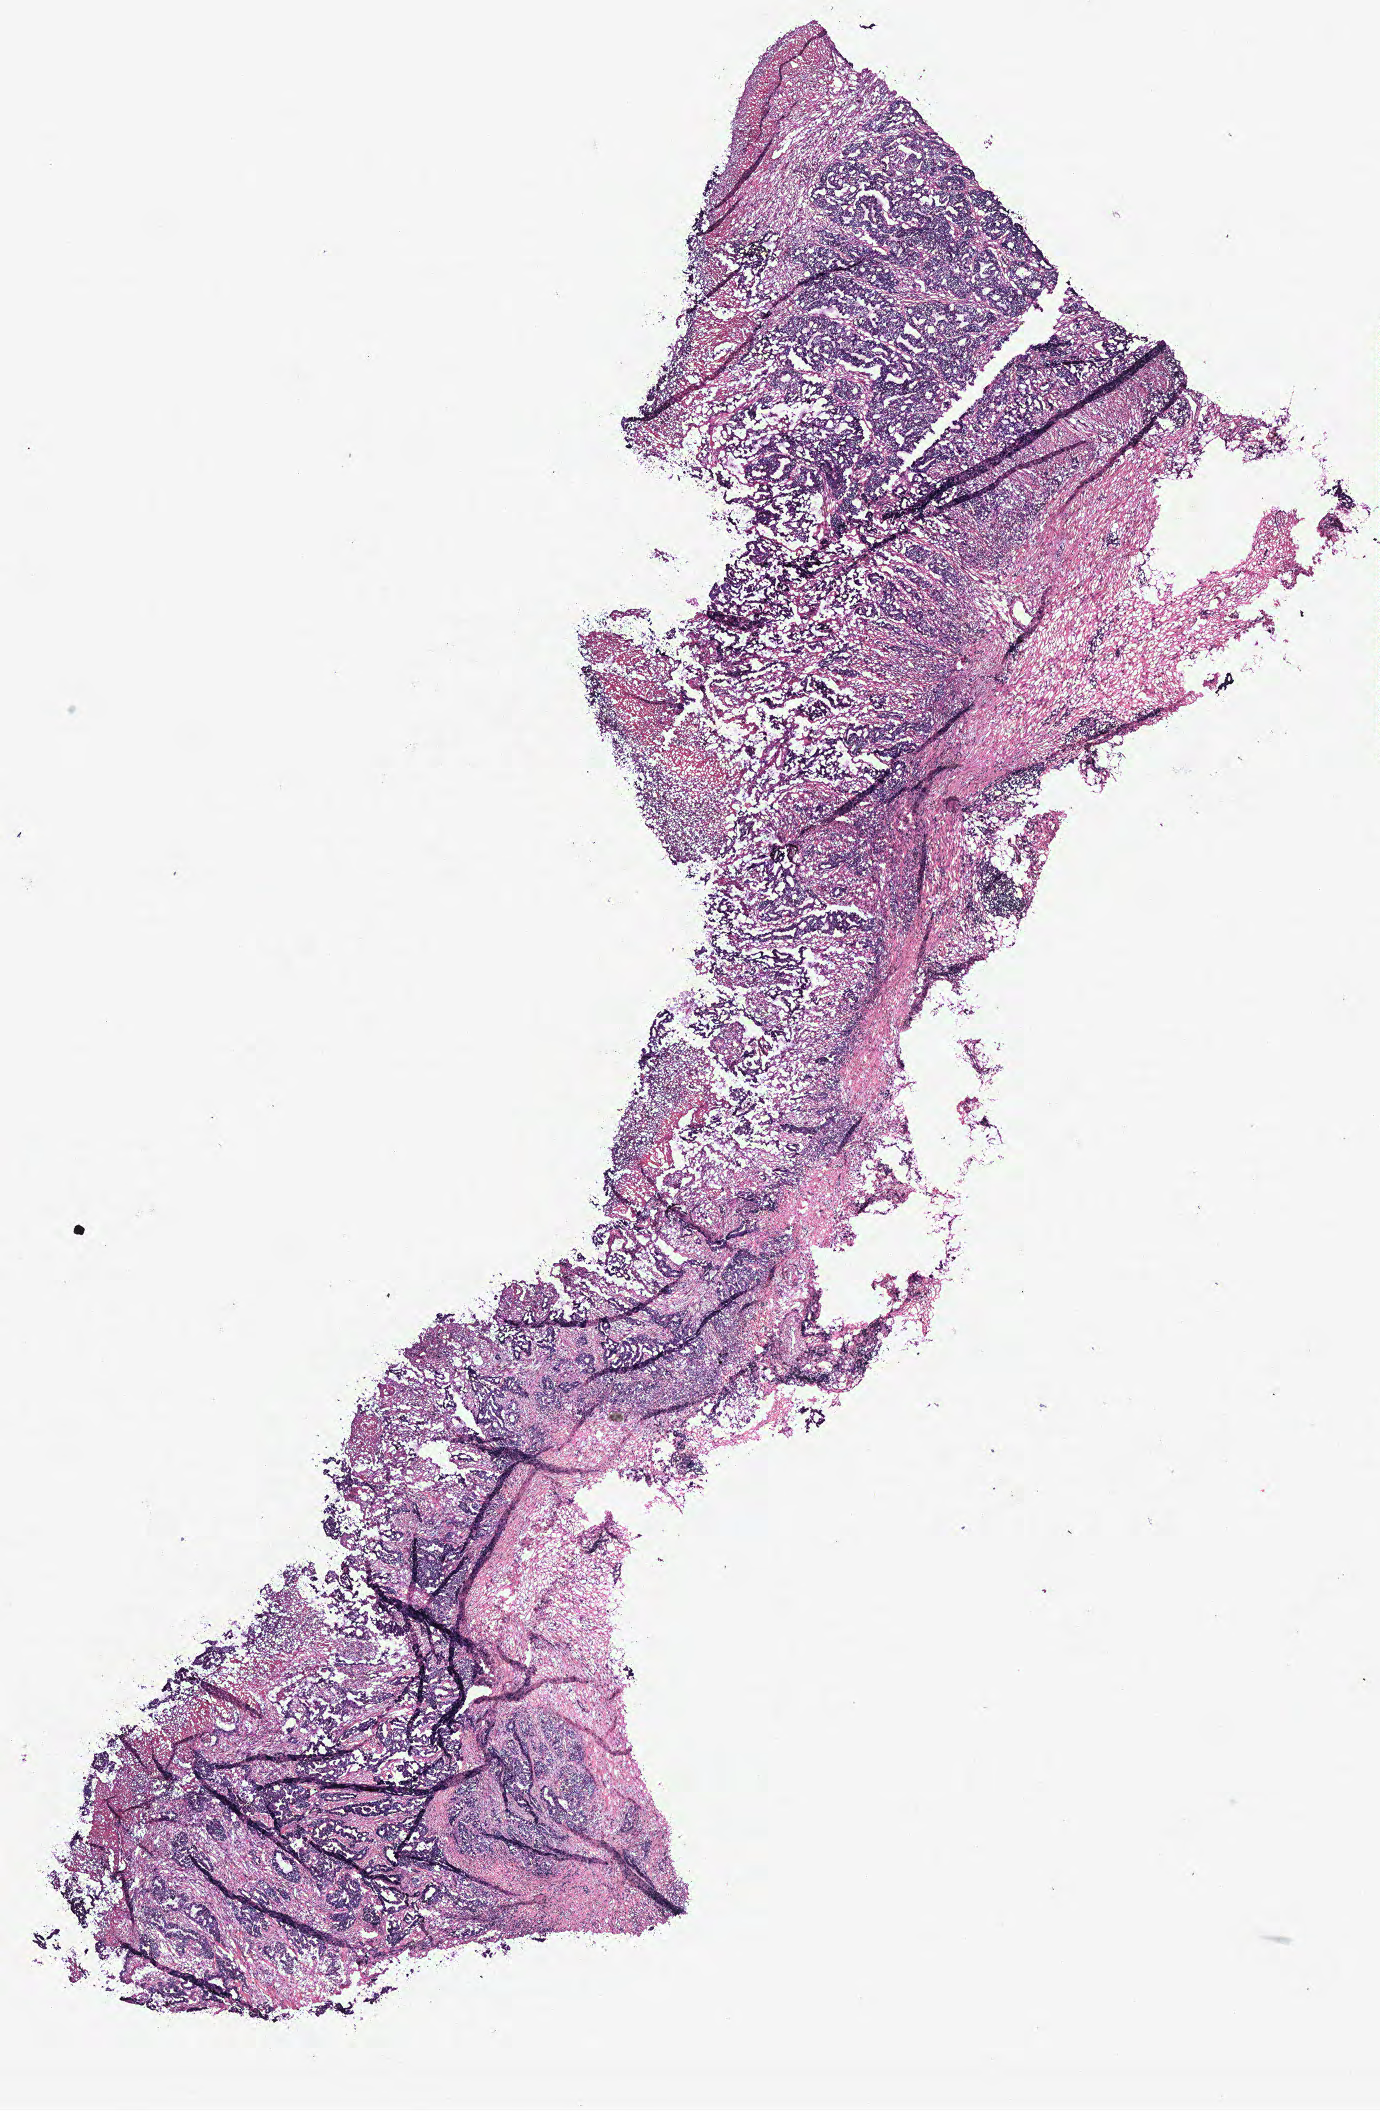
Digitized Hematoxylin and eosin (H&E) stained tissue section (whole slide) — shown as a low-resolution overview of the whole scanned area (about 11.0 x 16.9 mm). Colon, normal (non-tumour) tissue. 54-year-old female patient.
This section: normal (non-tumour) tissue from the same patient. Patient diagnosis: Adenocarcinoma, NOS.